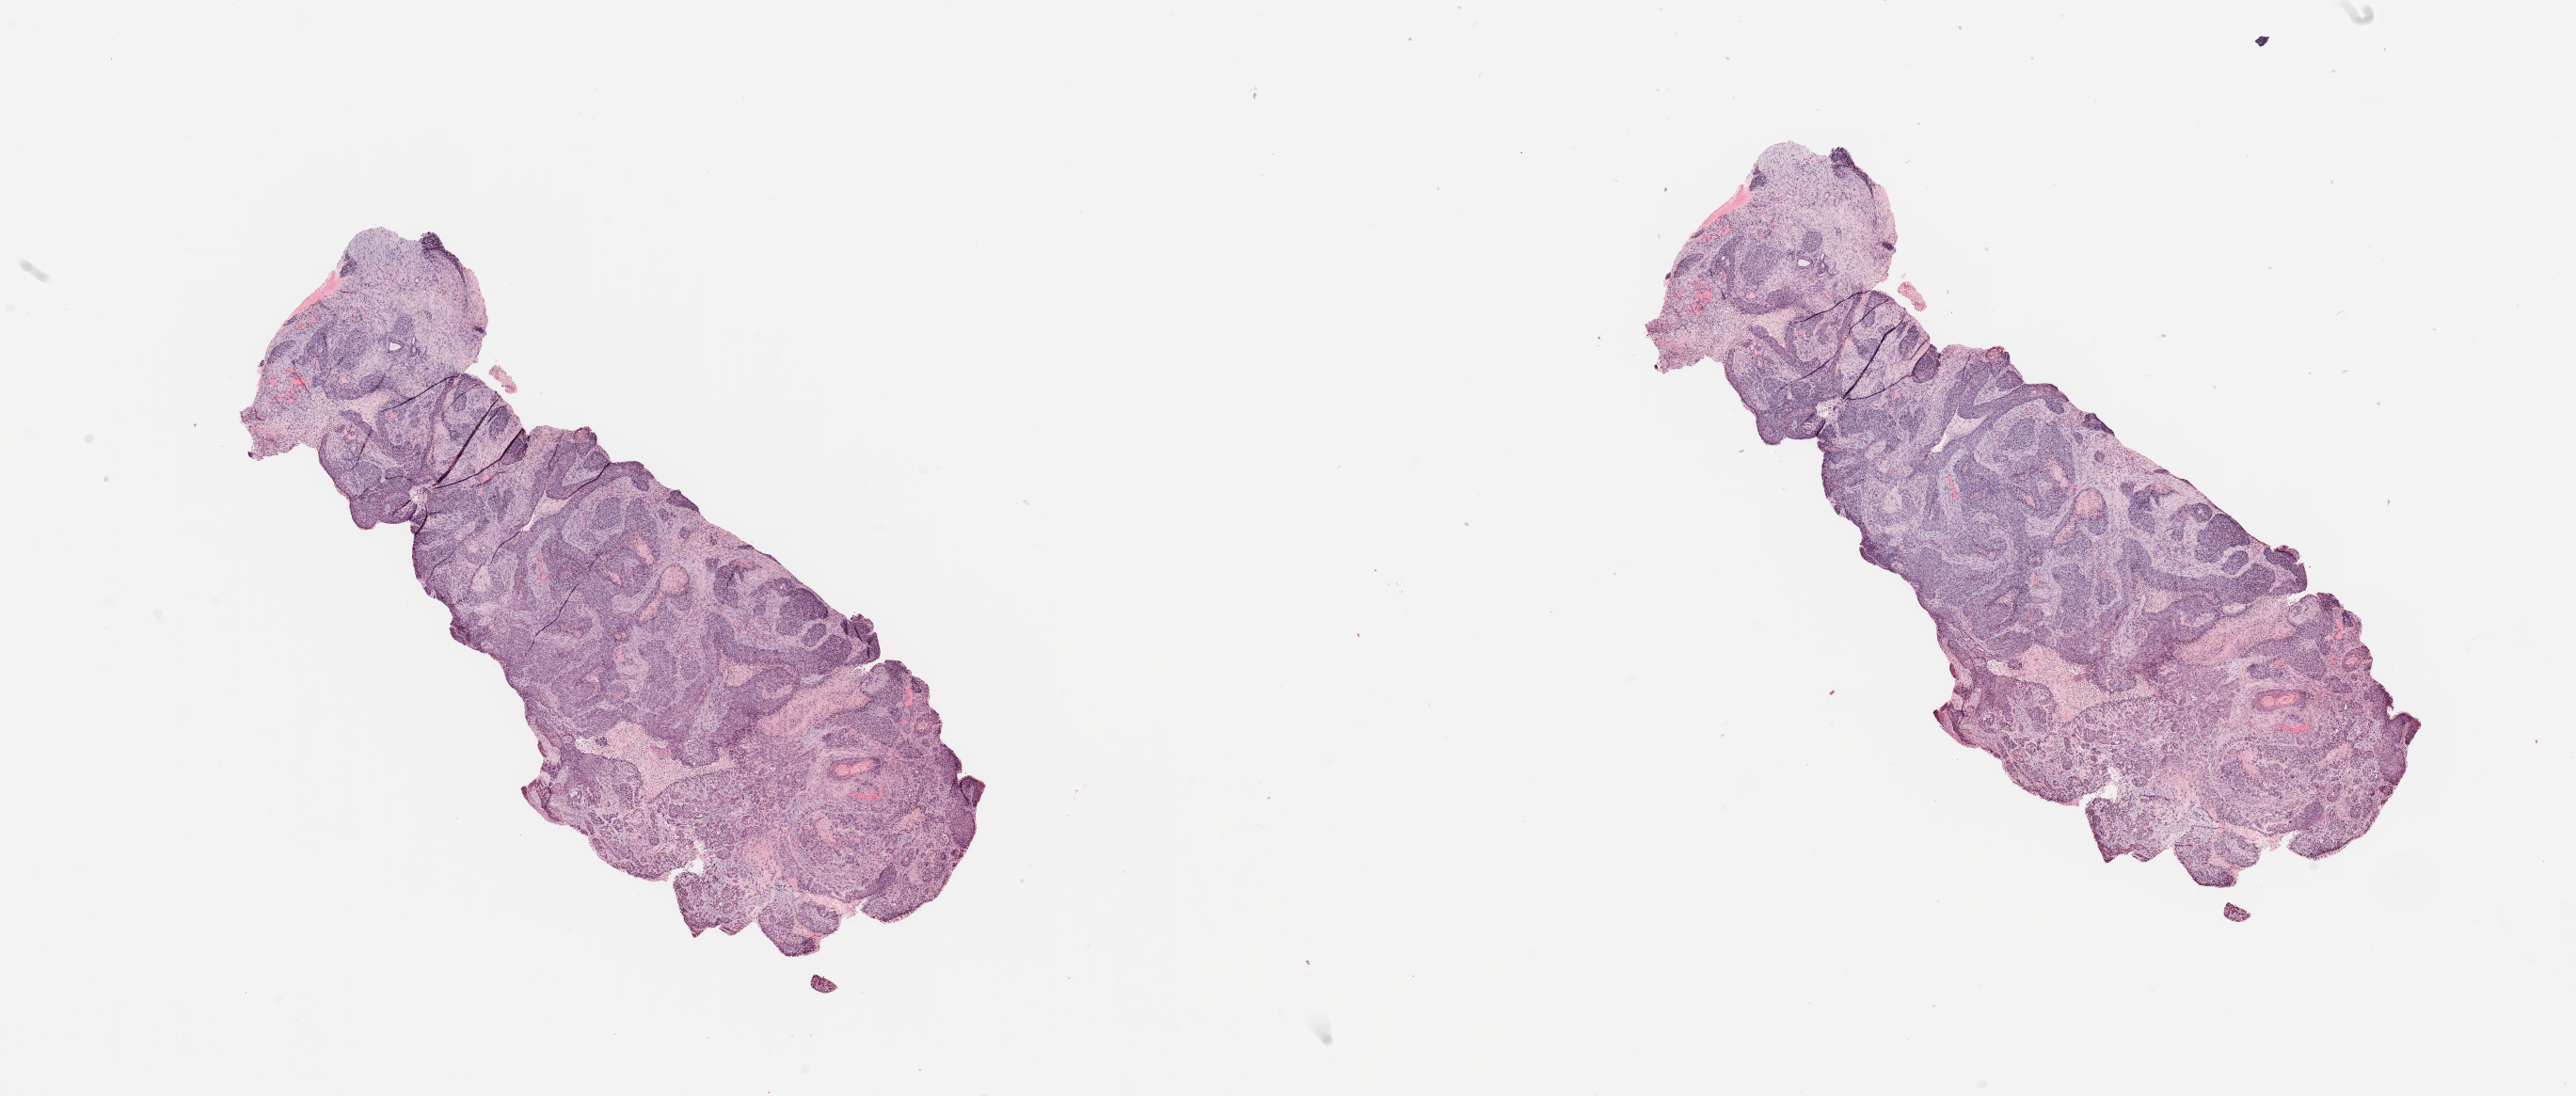
Whole-slide histology image, Hematoxylin and eosin (H&E) stained, low-resolution overview of the scanned area, about 21.7 x 9.2 mm (acquisition: 20x scan), tumour tissue sample, sampled site: lung. Male, 61 y/o. Histologic grade: G2 (moderately differentiated). Composition of this section per pathologist review: tumour nuclei 70%, necrosis 5%.
Histologic diagnosis: Squamous cell carcinoma, NOS. AJCC pathologic stage: IA. Primary tumour site (as recorded): left lower lobe.